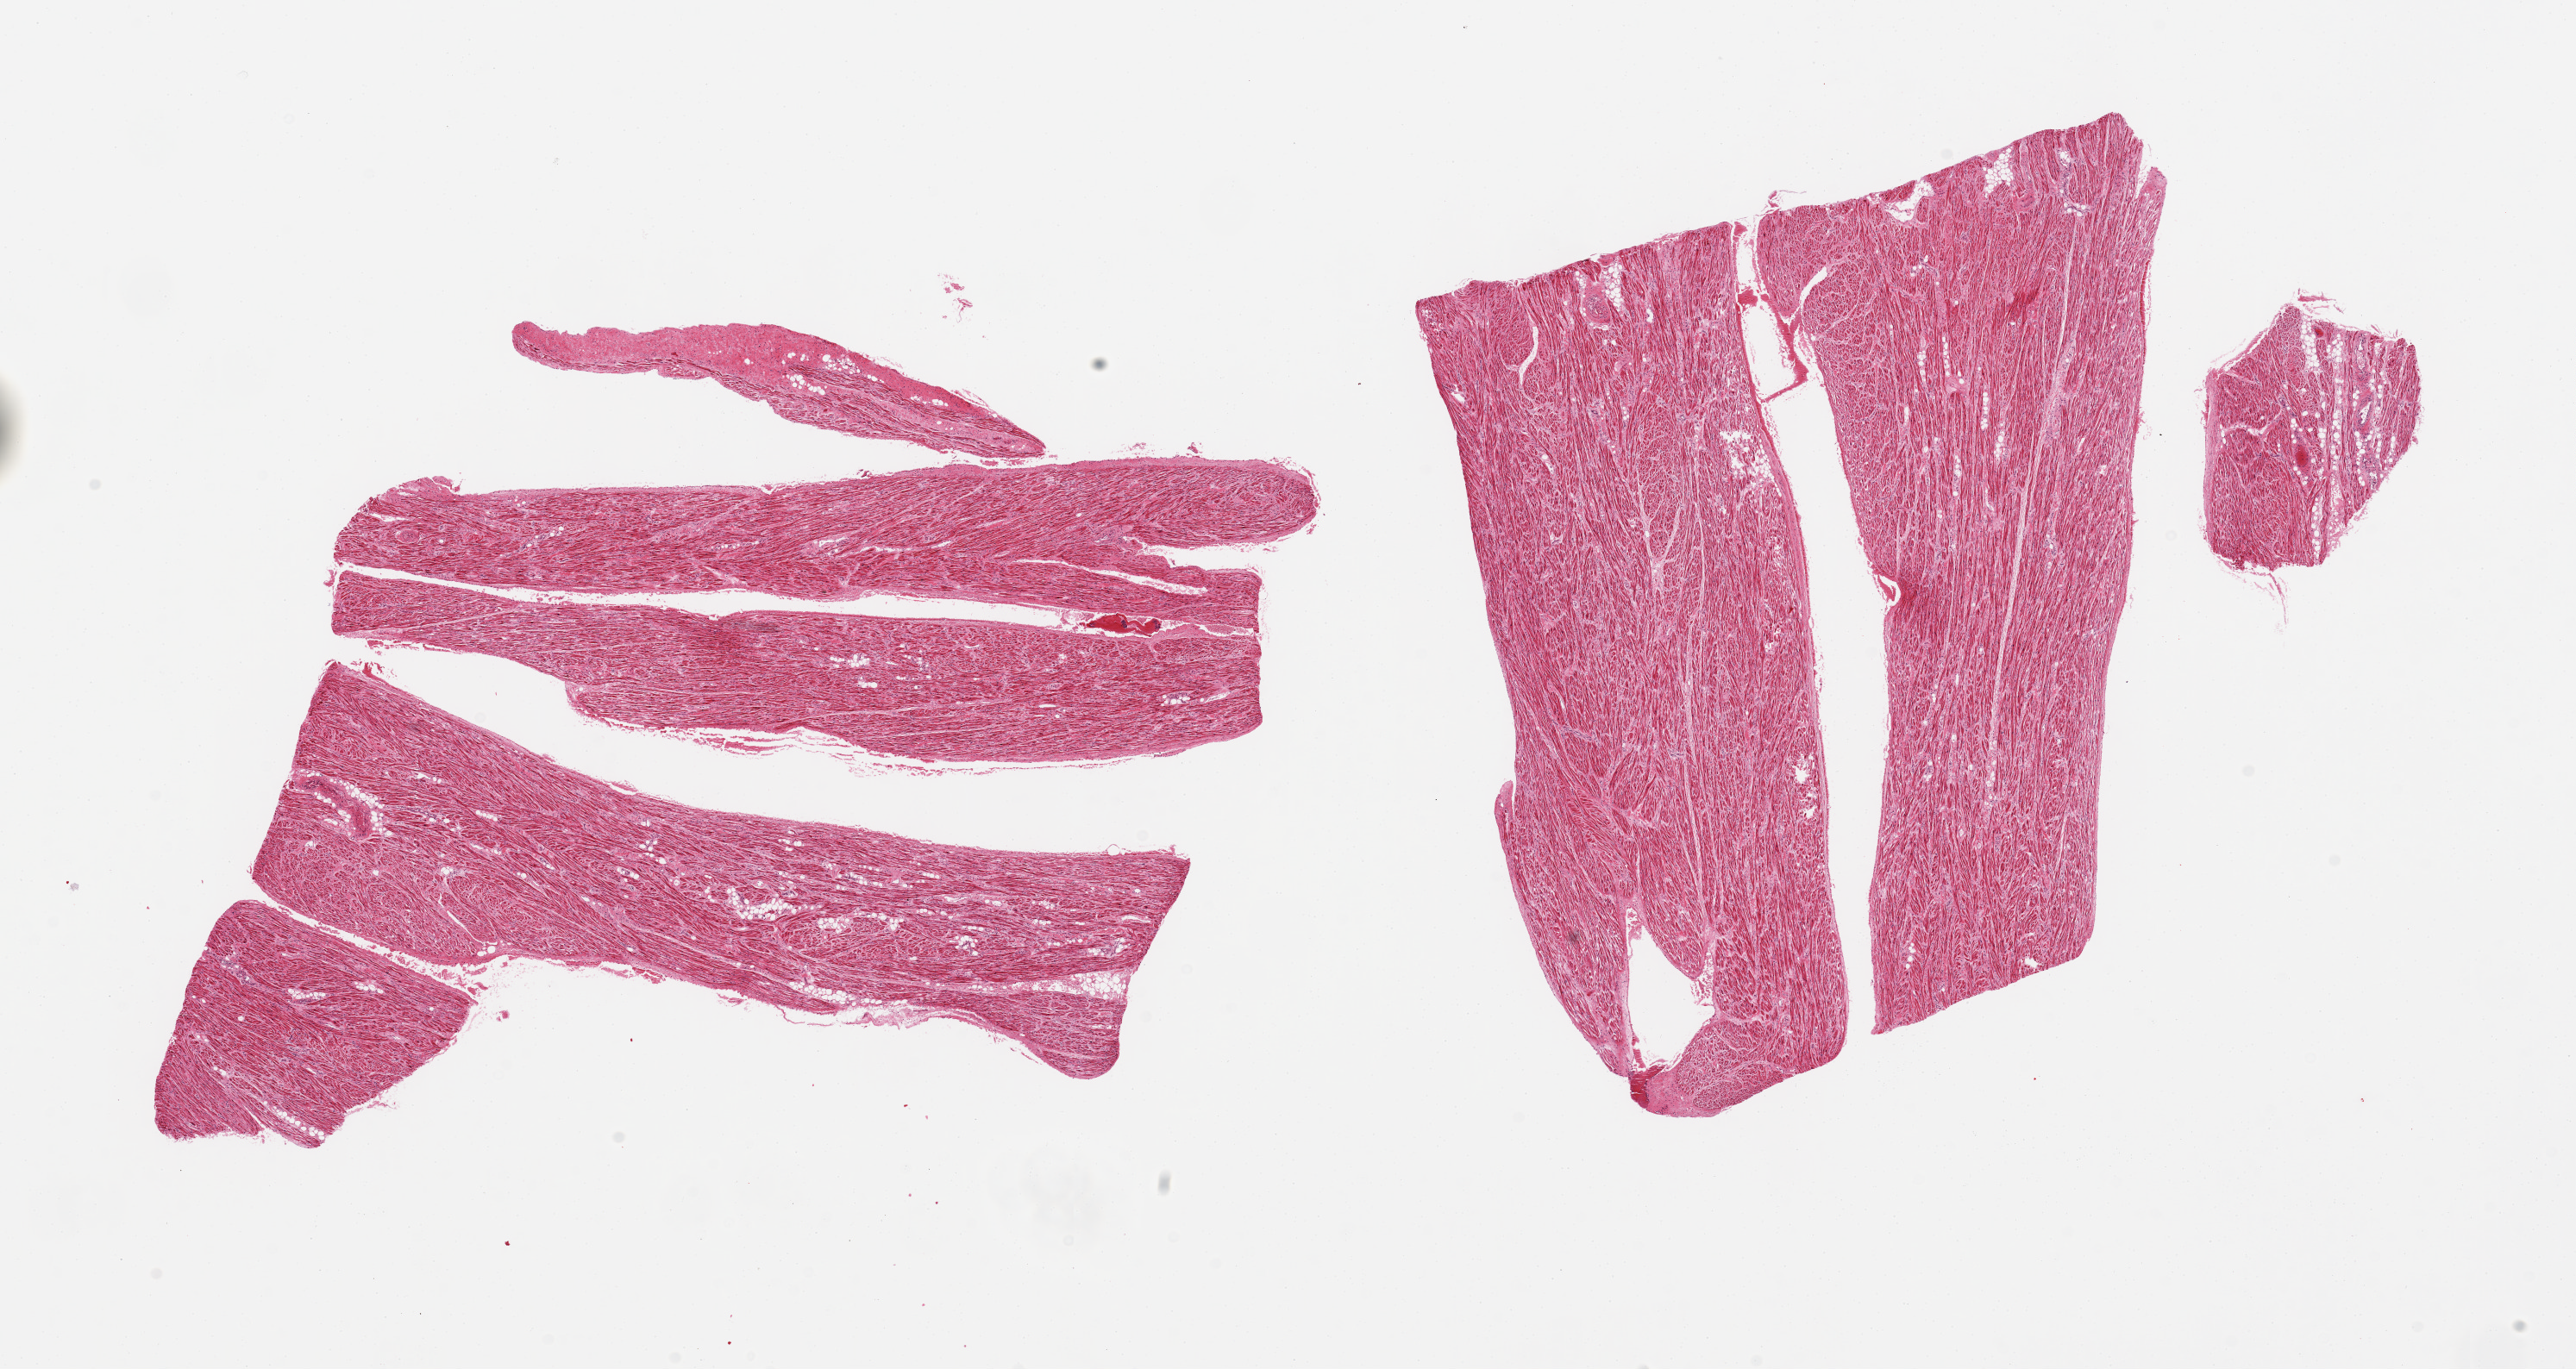
Whole-slide image, H&E stain — low-resolution overview of the scanned area, about 23.6 x 12.6 mm (slide scanned at 20x), PAXgene-fixed paraffin-embedded (PFPE) section, section of auricular appendage (target tissue), tissue donor sample. Donor: male.
- reviewer comment on this tissue sample: 2 pieces